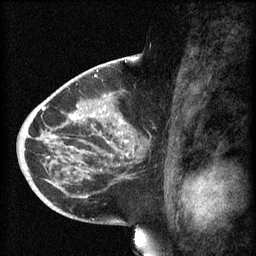
Breast MRI (dynamic contrast-enhanced), one sagittal slice; position 33 of 60 along the scan axis; 3 images stored at this slice position (order not interpretable as contrast timing); 1.5 T; TE 4.2 ms, TR 8.1 ms; 2 mm slice thickness; 256 × 256 image matrix, field of view 200 × 200 mm. Patient: female, 44 years.
Structures marked on this image (semi-automatically segmented with operator editing):
- analysis volume of interest (the breast-tissue region the enhancement analysis was run in; not a lesion): bounding box (x1, y1, x2, y2) in pixels: (59, 110, 150, 169)
- tumour enhancement mask (voxels above the 70 % enhancement threshold inside the analysis volume of interest): (70, 116, 128, 157)